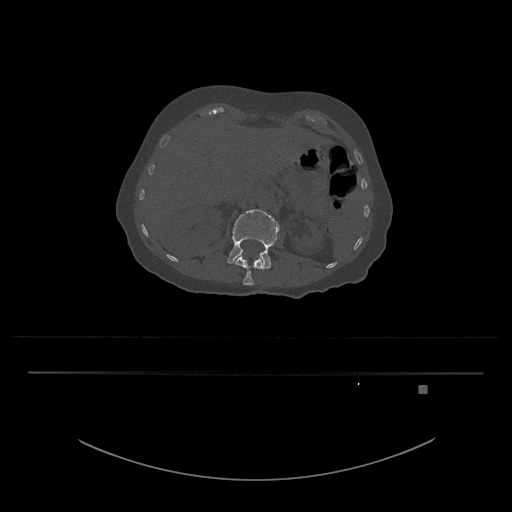
CT including the spine, one axial slice; slice 518 of 797 in the series (ordered by position); reconstruction kernel Br40s/3; bone window (W 1800 / L 400 HU); 0.5 mm slice thickness; 512 × 512 image matrix. Patient: female, 57 years. From the clinical record (not read from this slice): primary cancer: cervical.
Structures marked on this image (semi-automatic segmentation, software-assisted and operator-edited):
- L1 vertebra: bounding box (x1, y1, x2, y2) in pixels: (235, 255, 263, 285)